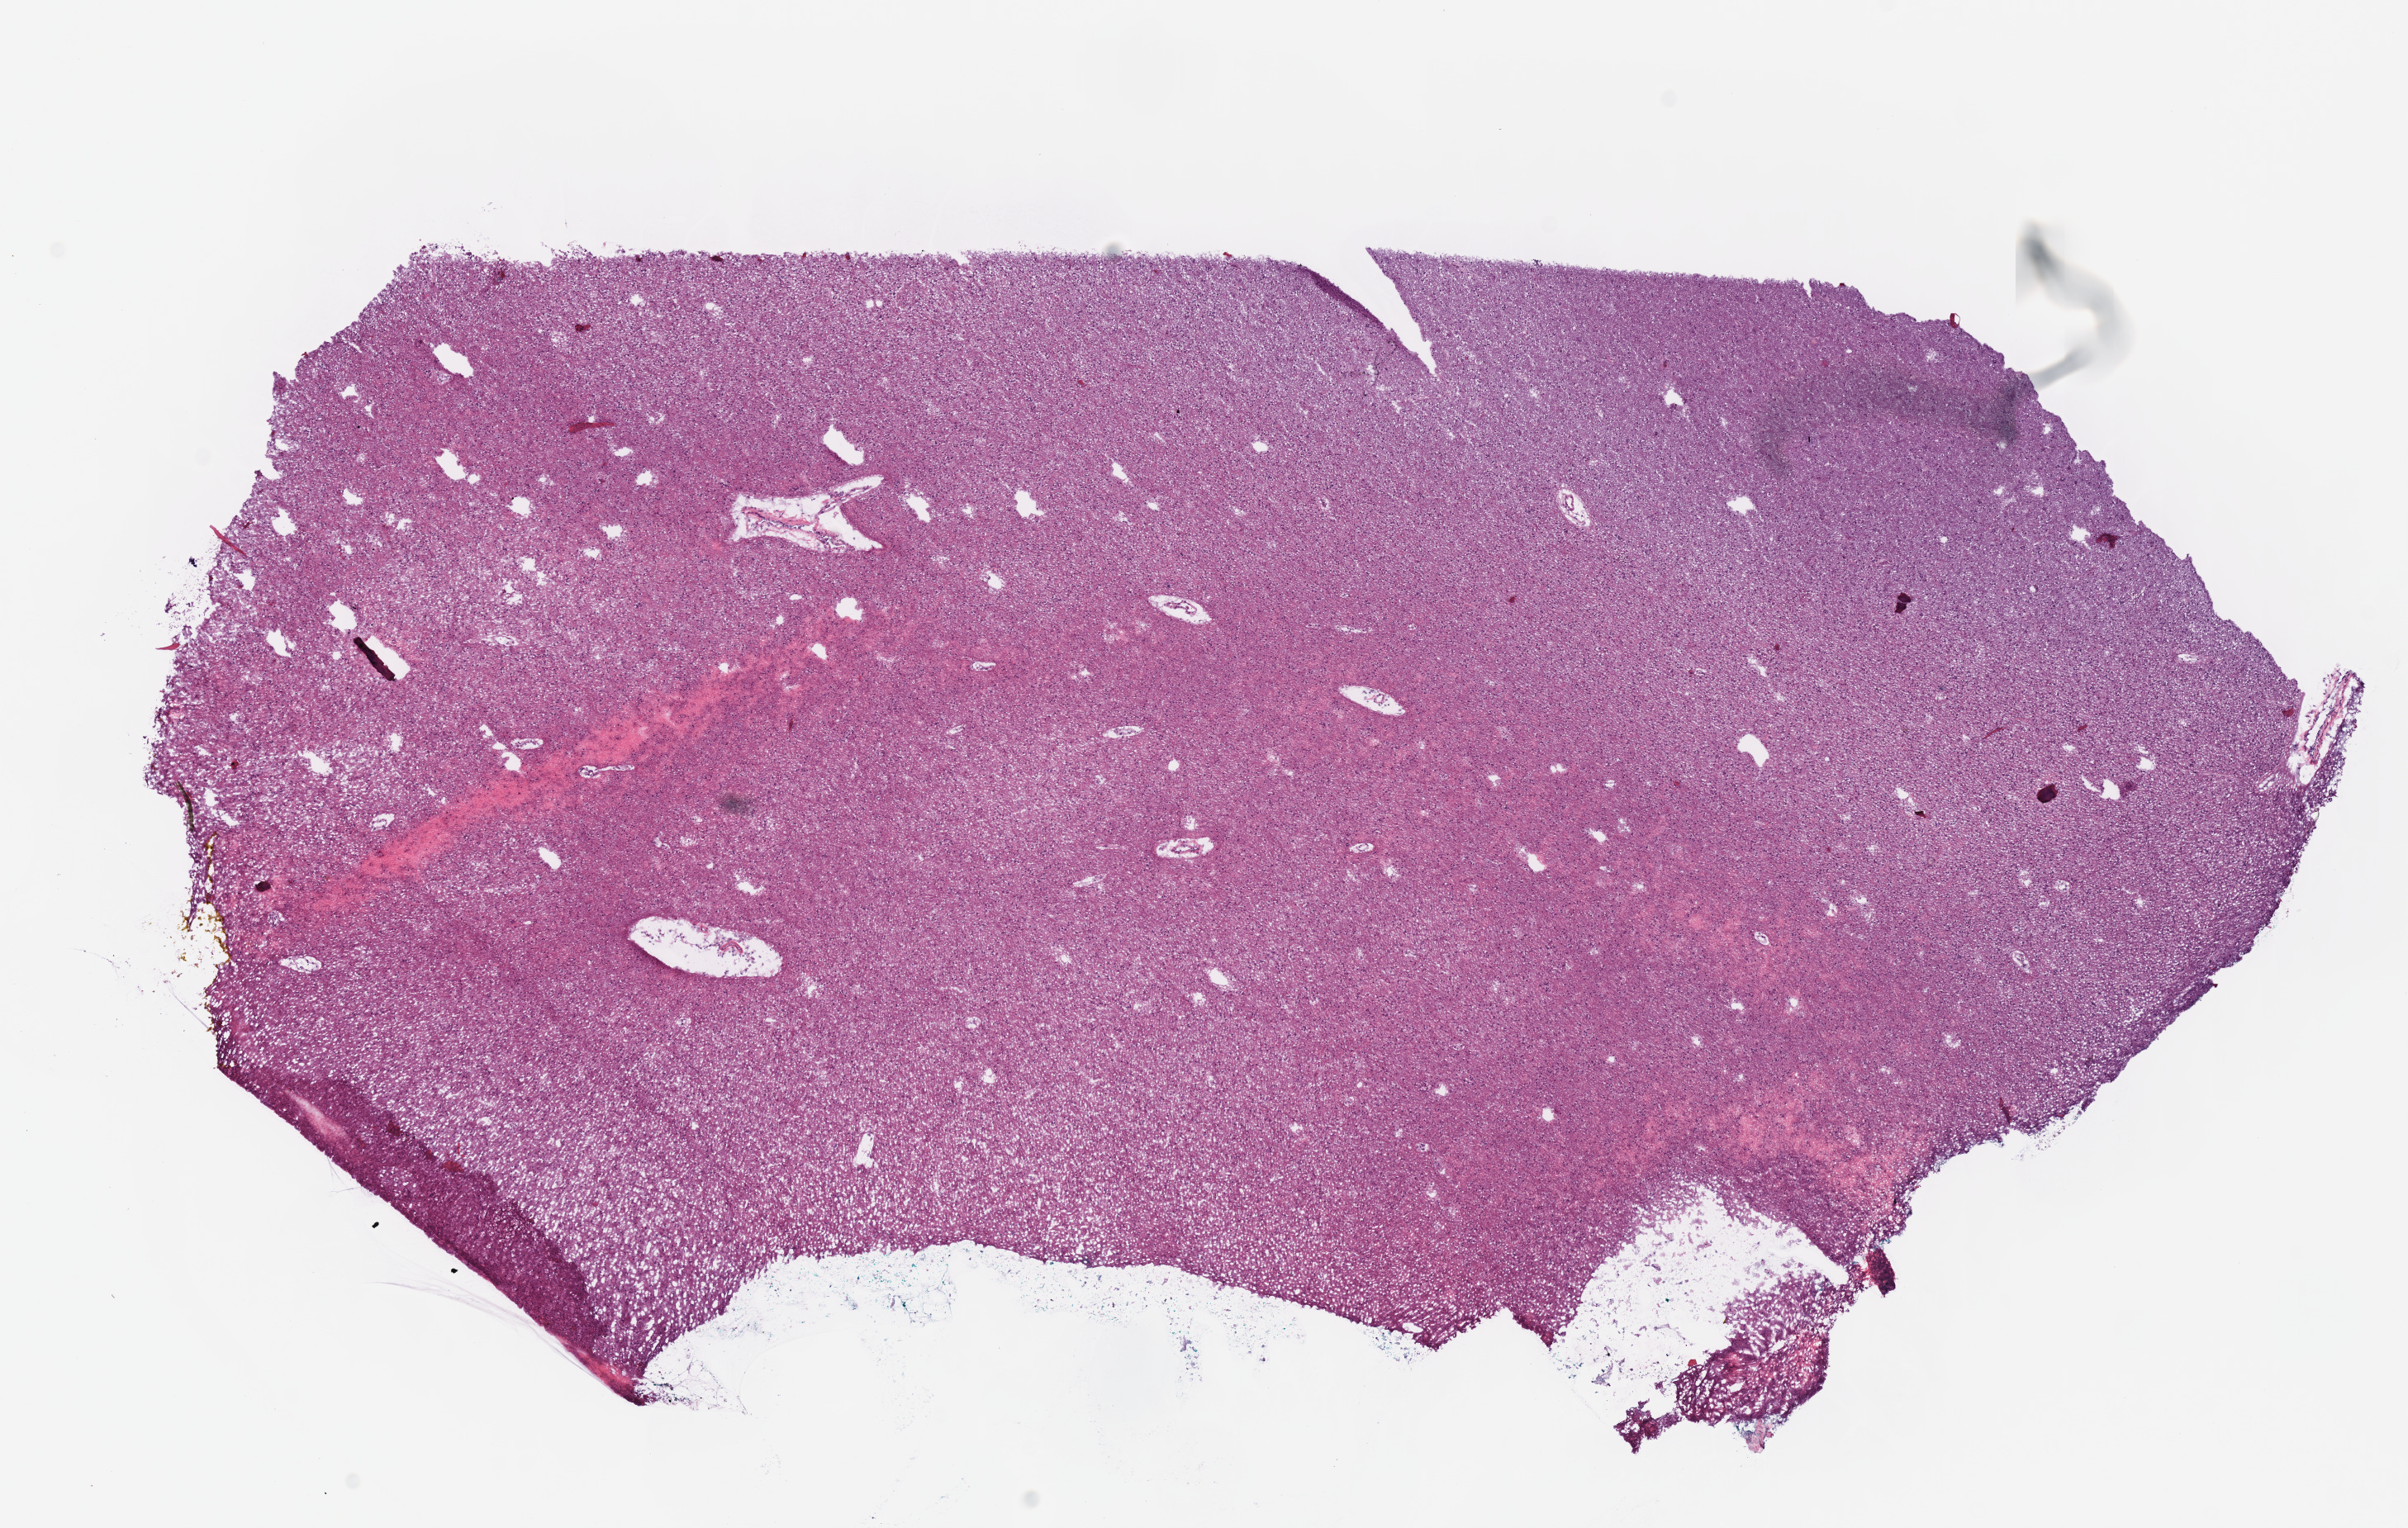
Hematoxylin and eosin (H&E) stained whole-slide image, low-resolution overview of the scanned area, about 11.5 x 7.3 mm (slide scanned at 40x), frozen section, primary tumour sample from the brain. Male, age 38 years at initial diagnosis. Histologic grade: G2 (moderately differentiated). Slide review estimates, as recorded: tumour cells 100%, tumour nuclei 60%, normal cells 0%, stromal cells 0%, necrosis 0%.
Histologic diagnosis: Oligodendroglioma, NOS.